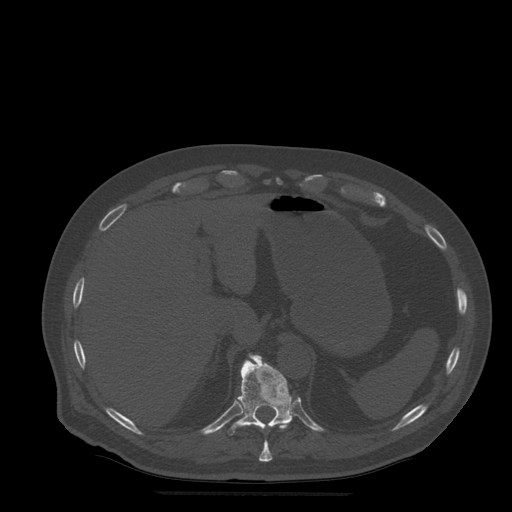
CT including the spine, one axial slice. Slice 252 of 522 in the series (ordered by position). Bone window (W 1800 / L 400 HU). 1.25 mm slice thickness. 512 × 512 image matrix, field of view 420 × 420 mm. Patient age 72 years. From the clinical record (not read from this slice): primary cancer: prostate.
Outlined on this slice (semi-automatically segmented with operator editing):
- T10 vertebra: box from (x=240, y=423) to (x=290, y=462) px
- T11 vertebra: (x=228, y=354)–(x=295, y=436)